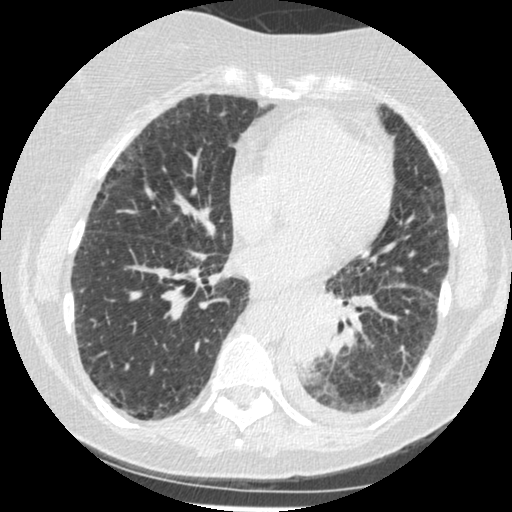
Chest CT (low-dose screening protocol), one axial image; third screening round (two years after baseline); lung window (W 1500 / L -600 HU); 1.25 mm slice thickness; slice 248 of 341 in the series; 512 × 512 image matrix. Female, age 60 years at enrolment.
- Lesion marked by an expert reader, box from (x=277, y=302) to (x=343, y=376) px.
- The exam's reader record, not a measurement of the box and not confirmed to be the same lesion: non-calcified nodule or mass ≥4 mm, left lower lobe, 54 × 38 mm, smooth margins, soft tissue attenuation, pre-existing on the prior screen: yes; interval growth: yes.
- Later outcome: lung cancer diagnosed 15 days after this screen — small cell carcinoma, NOS, left lower lobe, undifferentiated (G4), stage IV (AJCC 6th edition), 69 mm at pathology.